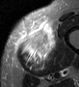
MRI of an extremity soft-tissue mass, one axial slice. Slice 13 of 45 in the series (ordered by position). STIR. MR volume resampled by the dataset authors to the PET/CT grid (not the native acquisition matrix). 3.27 mm slice thickness. 79 × 87 image matrix, field of view 77 × 85 mm. Male patient. Case-level facts recorded for this patient, not image findings: histological type: pleiomorphic leiomyosarcoma; grade: high; site of the primary tumour: left thigh.
Annotated regions visible in this slice (expert contour drawn on MRI and transferred to this co-registered scan by the dataset authors):
- gross tumour volume including surrounding oedema: bounding box (x1, y1, x2, y2) in pixels: (18, 20, 58, 70)
- gross tumour volume (mass): (18, 23, 55, 58)